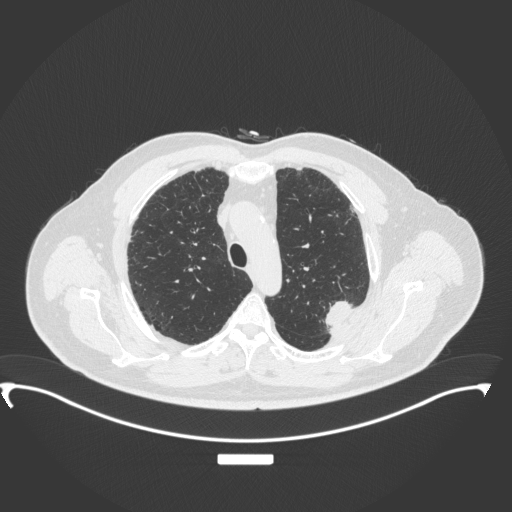
Chest CT, one axial slice. Position 274 of 350 along the scan axis. Lung window (W 1500 / L -600 HU). 512 × 512 image matrix, field of view 459 × 459 mm. Male patient, age 64 years. From the clinical record (not read from this slice): clinical TNM (as recorded): T1c N1 M1.
Outlined on this slice (bounding box drawn by a radiologist):
- lung tumour (recorded histology: adenocarcinoma): bounding box (x1, y1, x2, y2) in pixels: (319, 294, 355, 334)